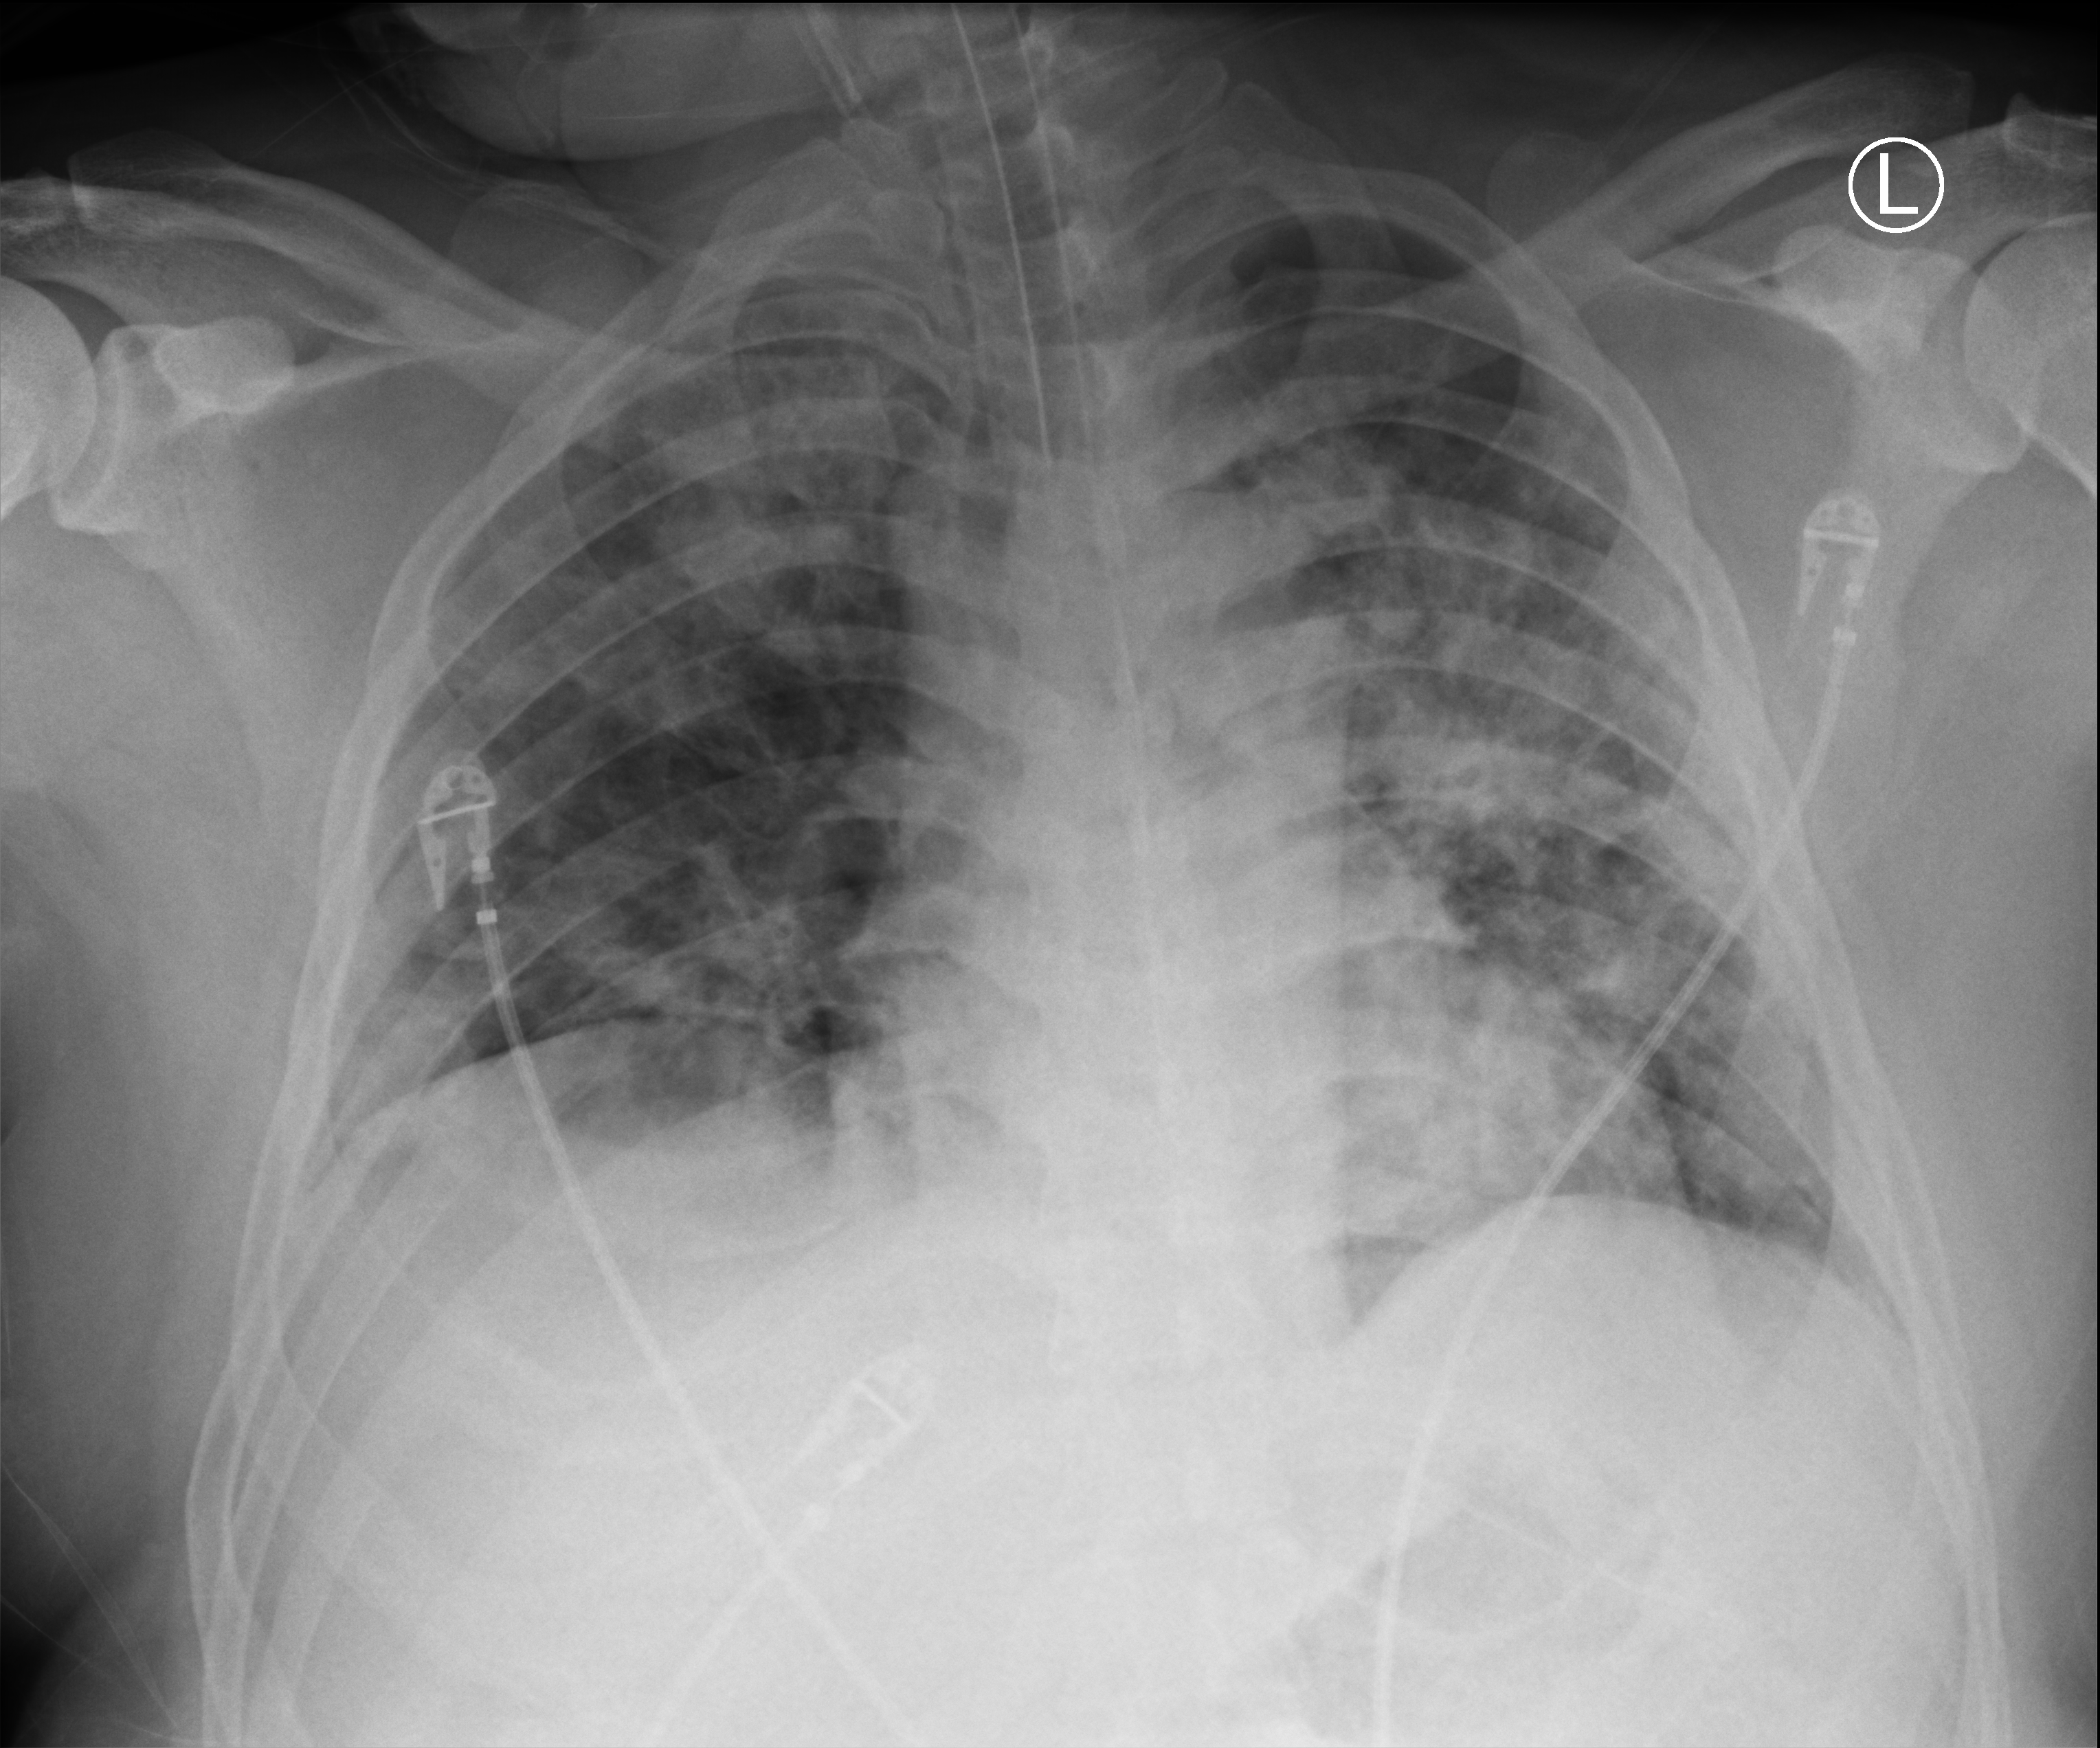
Chest X-ray (portable); anteroposterior (AP) projection. Patient hospitalised with COVID-19; male, aged 18–59 years.
Hospital-stay facts (about this admission, not read from this image; timing relative to this image not recorded): mechanically ventilated during this hospital stay: yes.